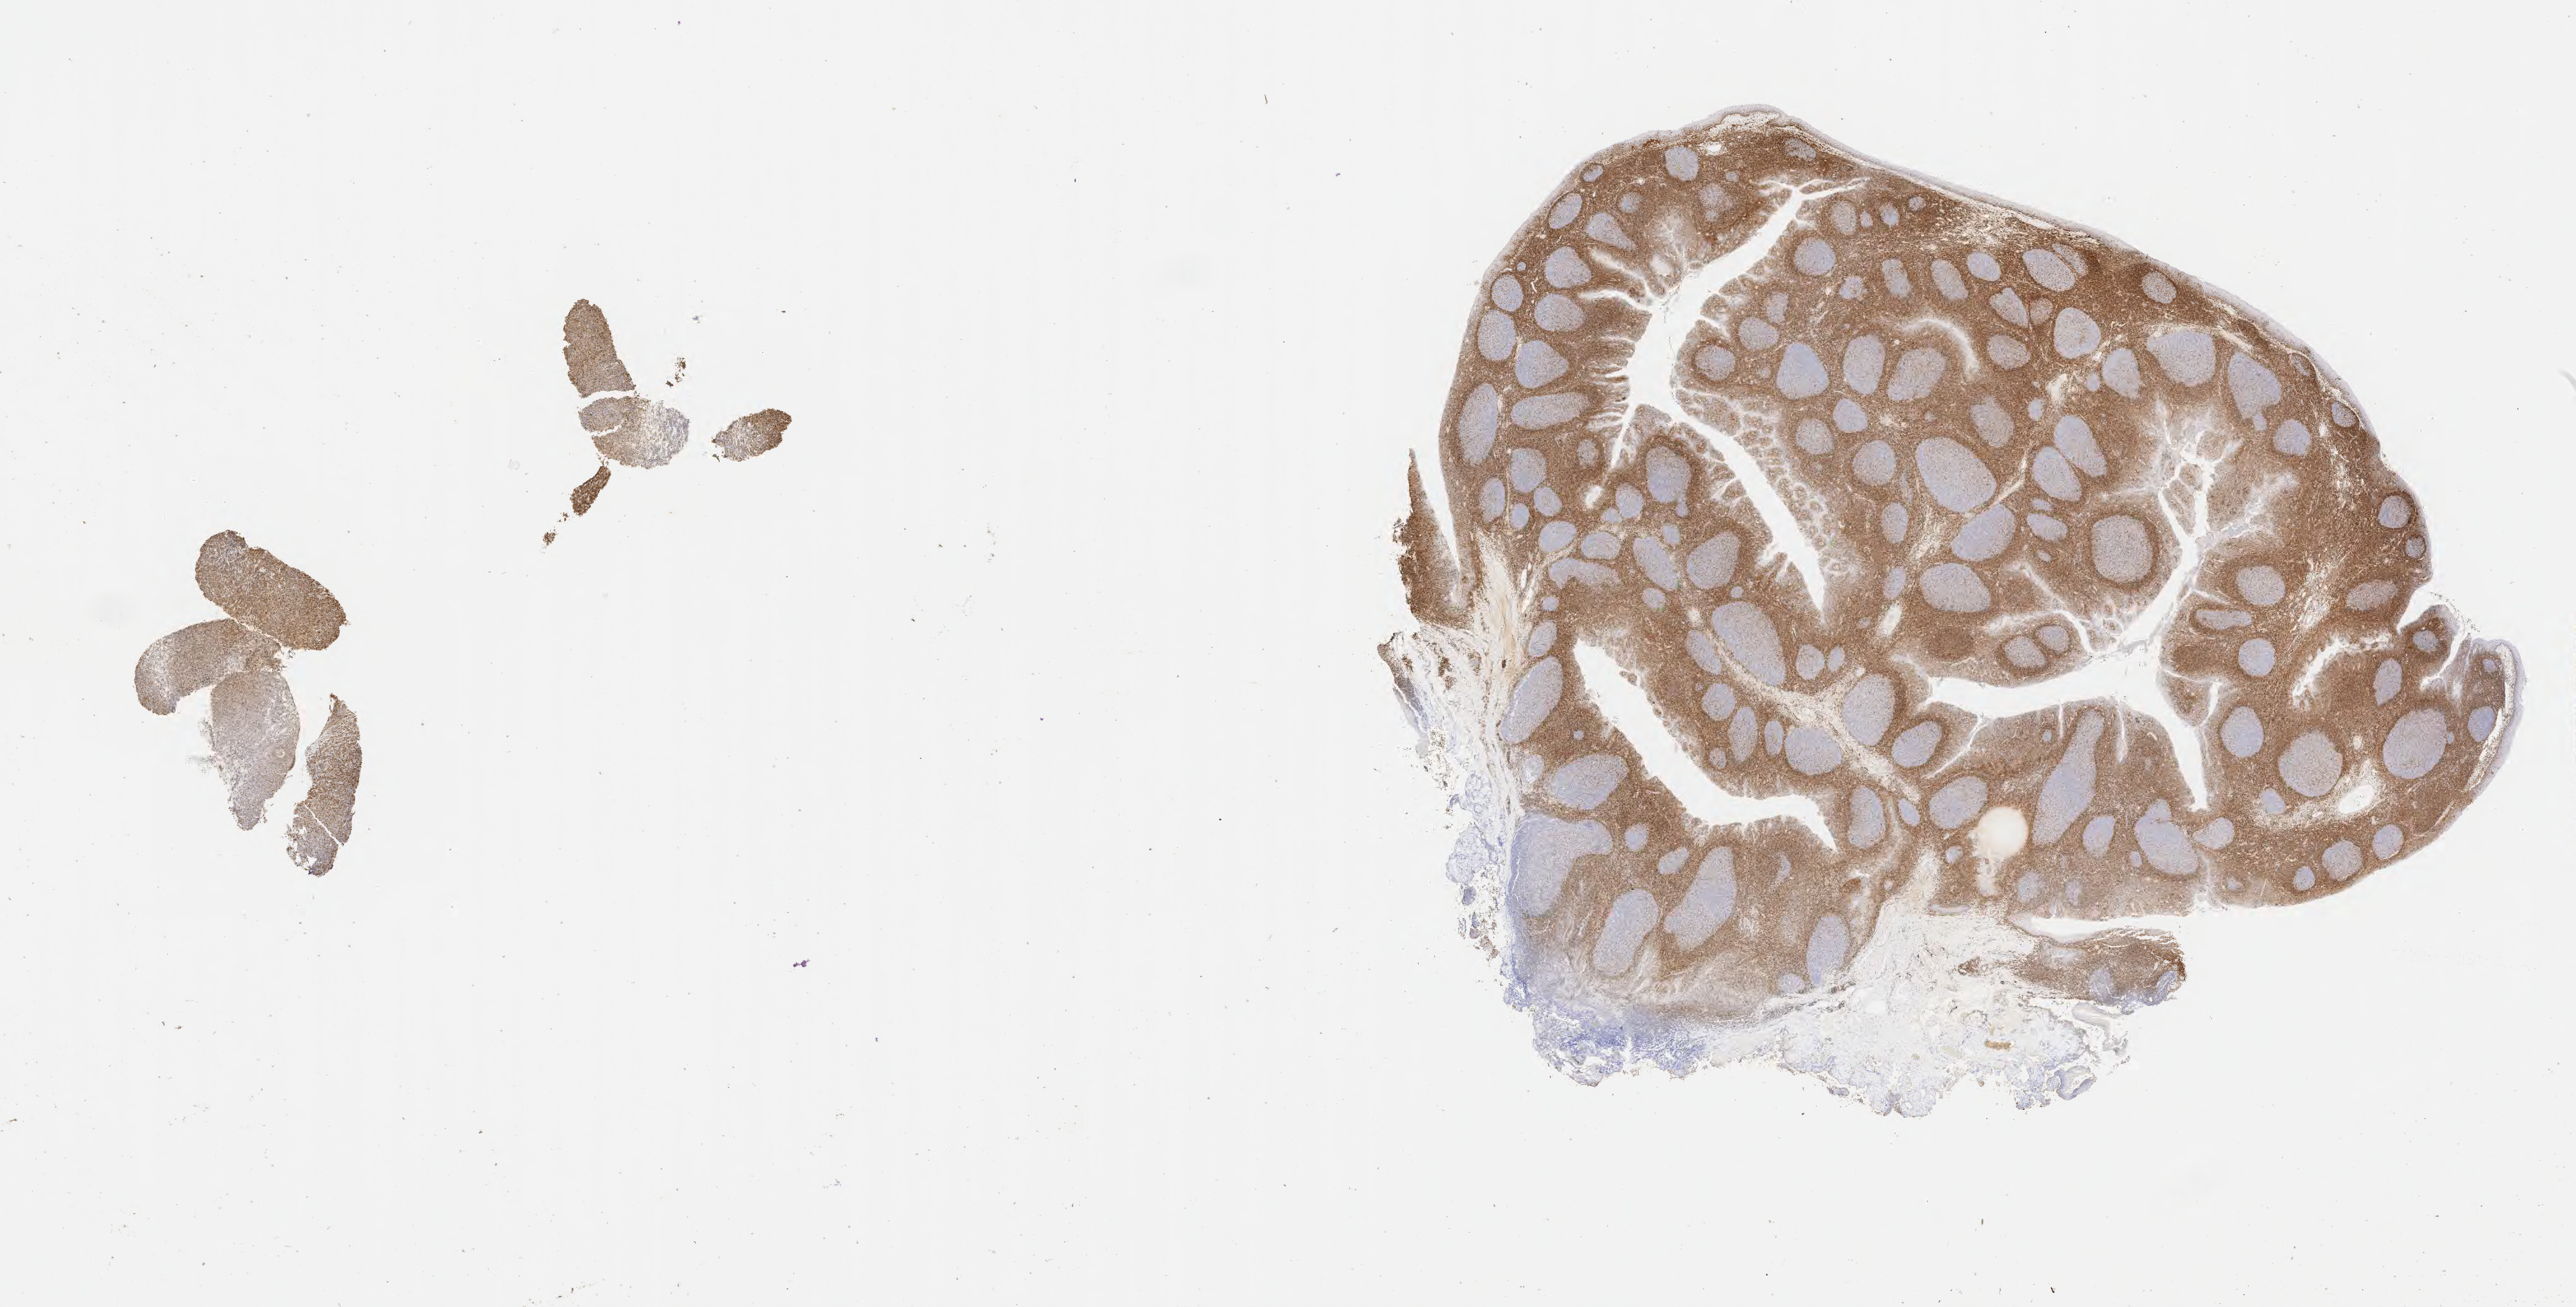
Immunohistochemistry (IHC) whole-slide image stained for BCL2, a low-resolution overview of the entire scanned area, about 32.7 x 16.6 mm; specimen: tumor tissue; site: lymph node. Patient: male, age 54 years.
Histologic diagnosis: Diffuse large B-cell lymphoma, NOS.